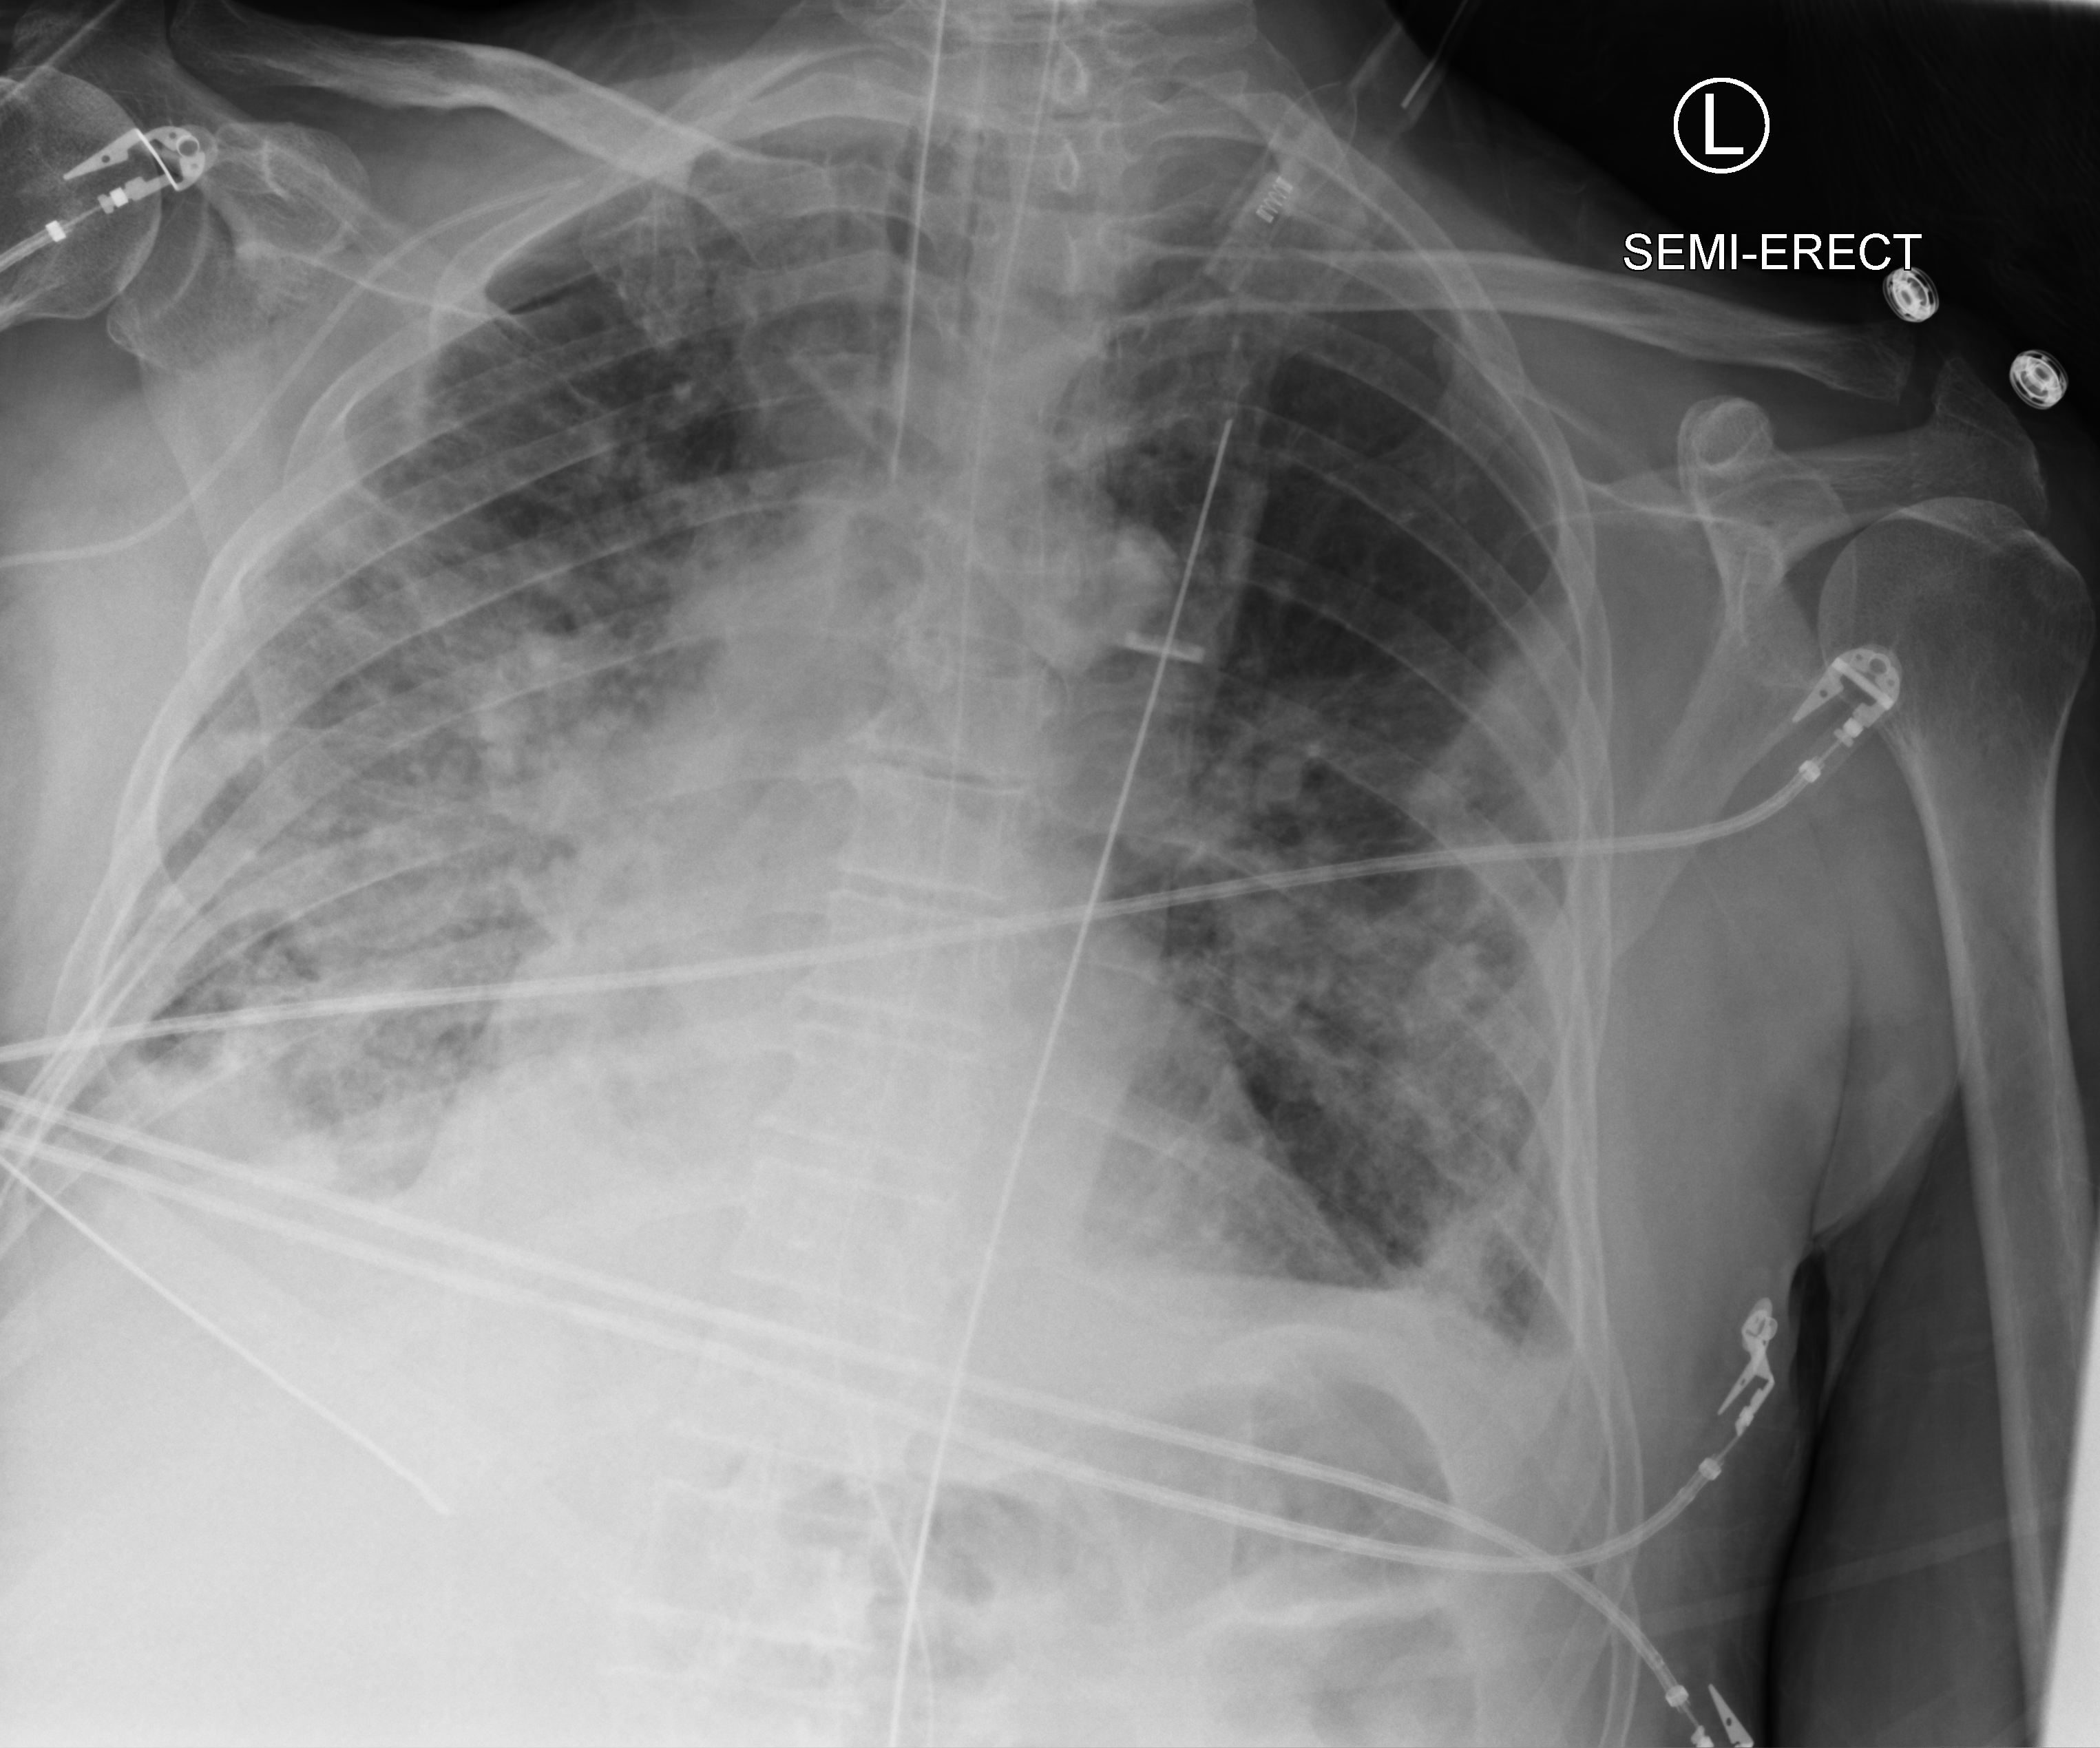
Portable chest radiograph, anteroposterior (AP) projection. Male patient hospitalised with COVID-19, age 75–90 years.
Admission-level facts for this patient (not findings on this image; timing relative to this image not recorded): COPD (admission record): no; admitted to intensive care during this hospital stay: yes.